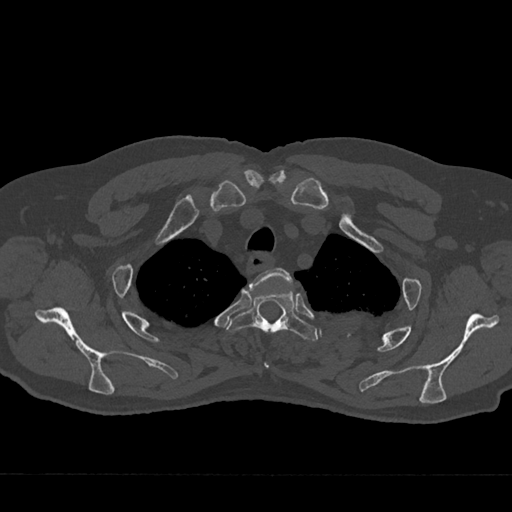
CT including the spine, one axial slice. Slice 579 of 797 in the series (ordered by position). Reconstruction kernel Br40s/3. Bone window (W 1800 / L 400 HU). 0.5 mm slice thickness. 512 × 512 image matrix, field of view 377 × 377 mm. Male patient, age 75 years. From the clinical record (not read from this slice): primary cancer: renal; vertebrae with lytic lesions (as recorded): T4.
Outlined on this slice (semi-automatically segmented with operator editing):
- T2 vertebra: box from (x=249, y=268) to (x=292, y=368) px
- T3 vertebra: (x=228, y=290)–(x=318, y=341)